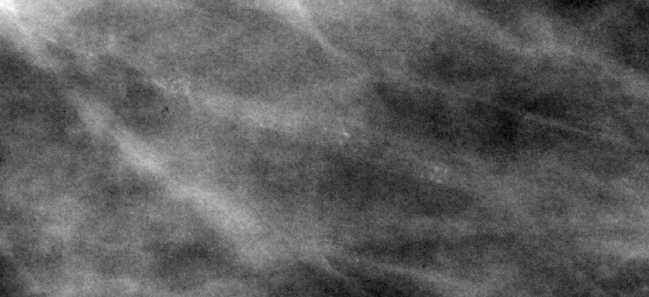
Crop from a digitized film mammogram around one marked abnormality; right breast; CC view; BI-RADS breast density category 3 (scale 1–4).
- Marked abnormality: calcifications, morphology vascular; BI-RADS assessment category 2; subtlety rating 3 on a 1 (subtle) to 5 (obvious) scale; benign; no additional work-up was recommended (benign without callback).